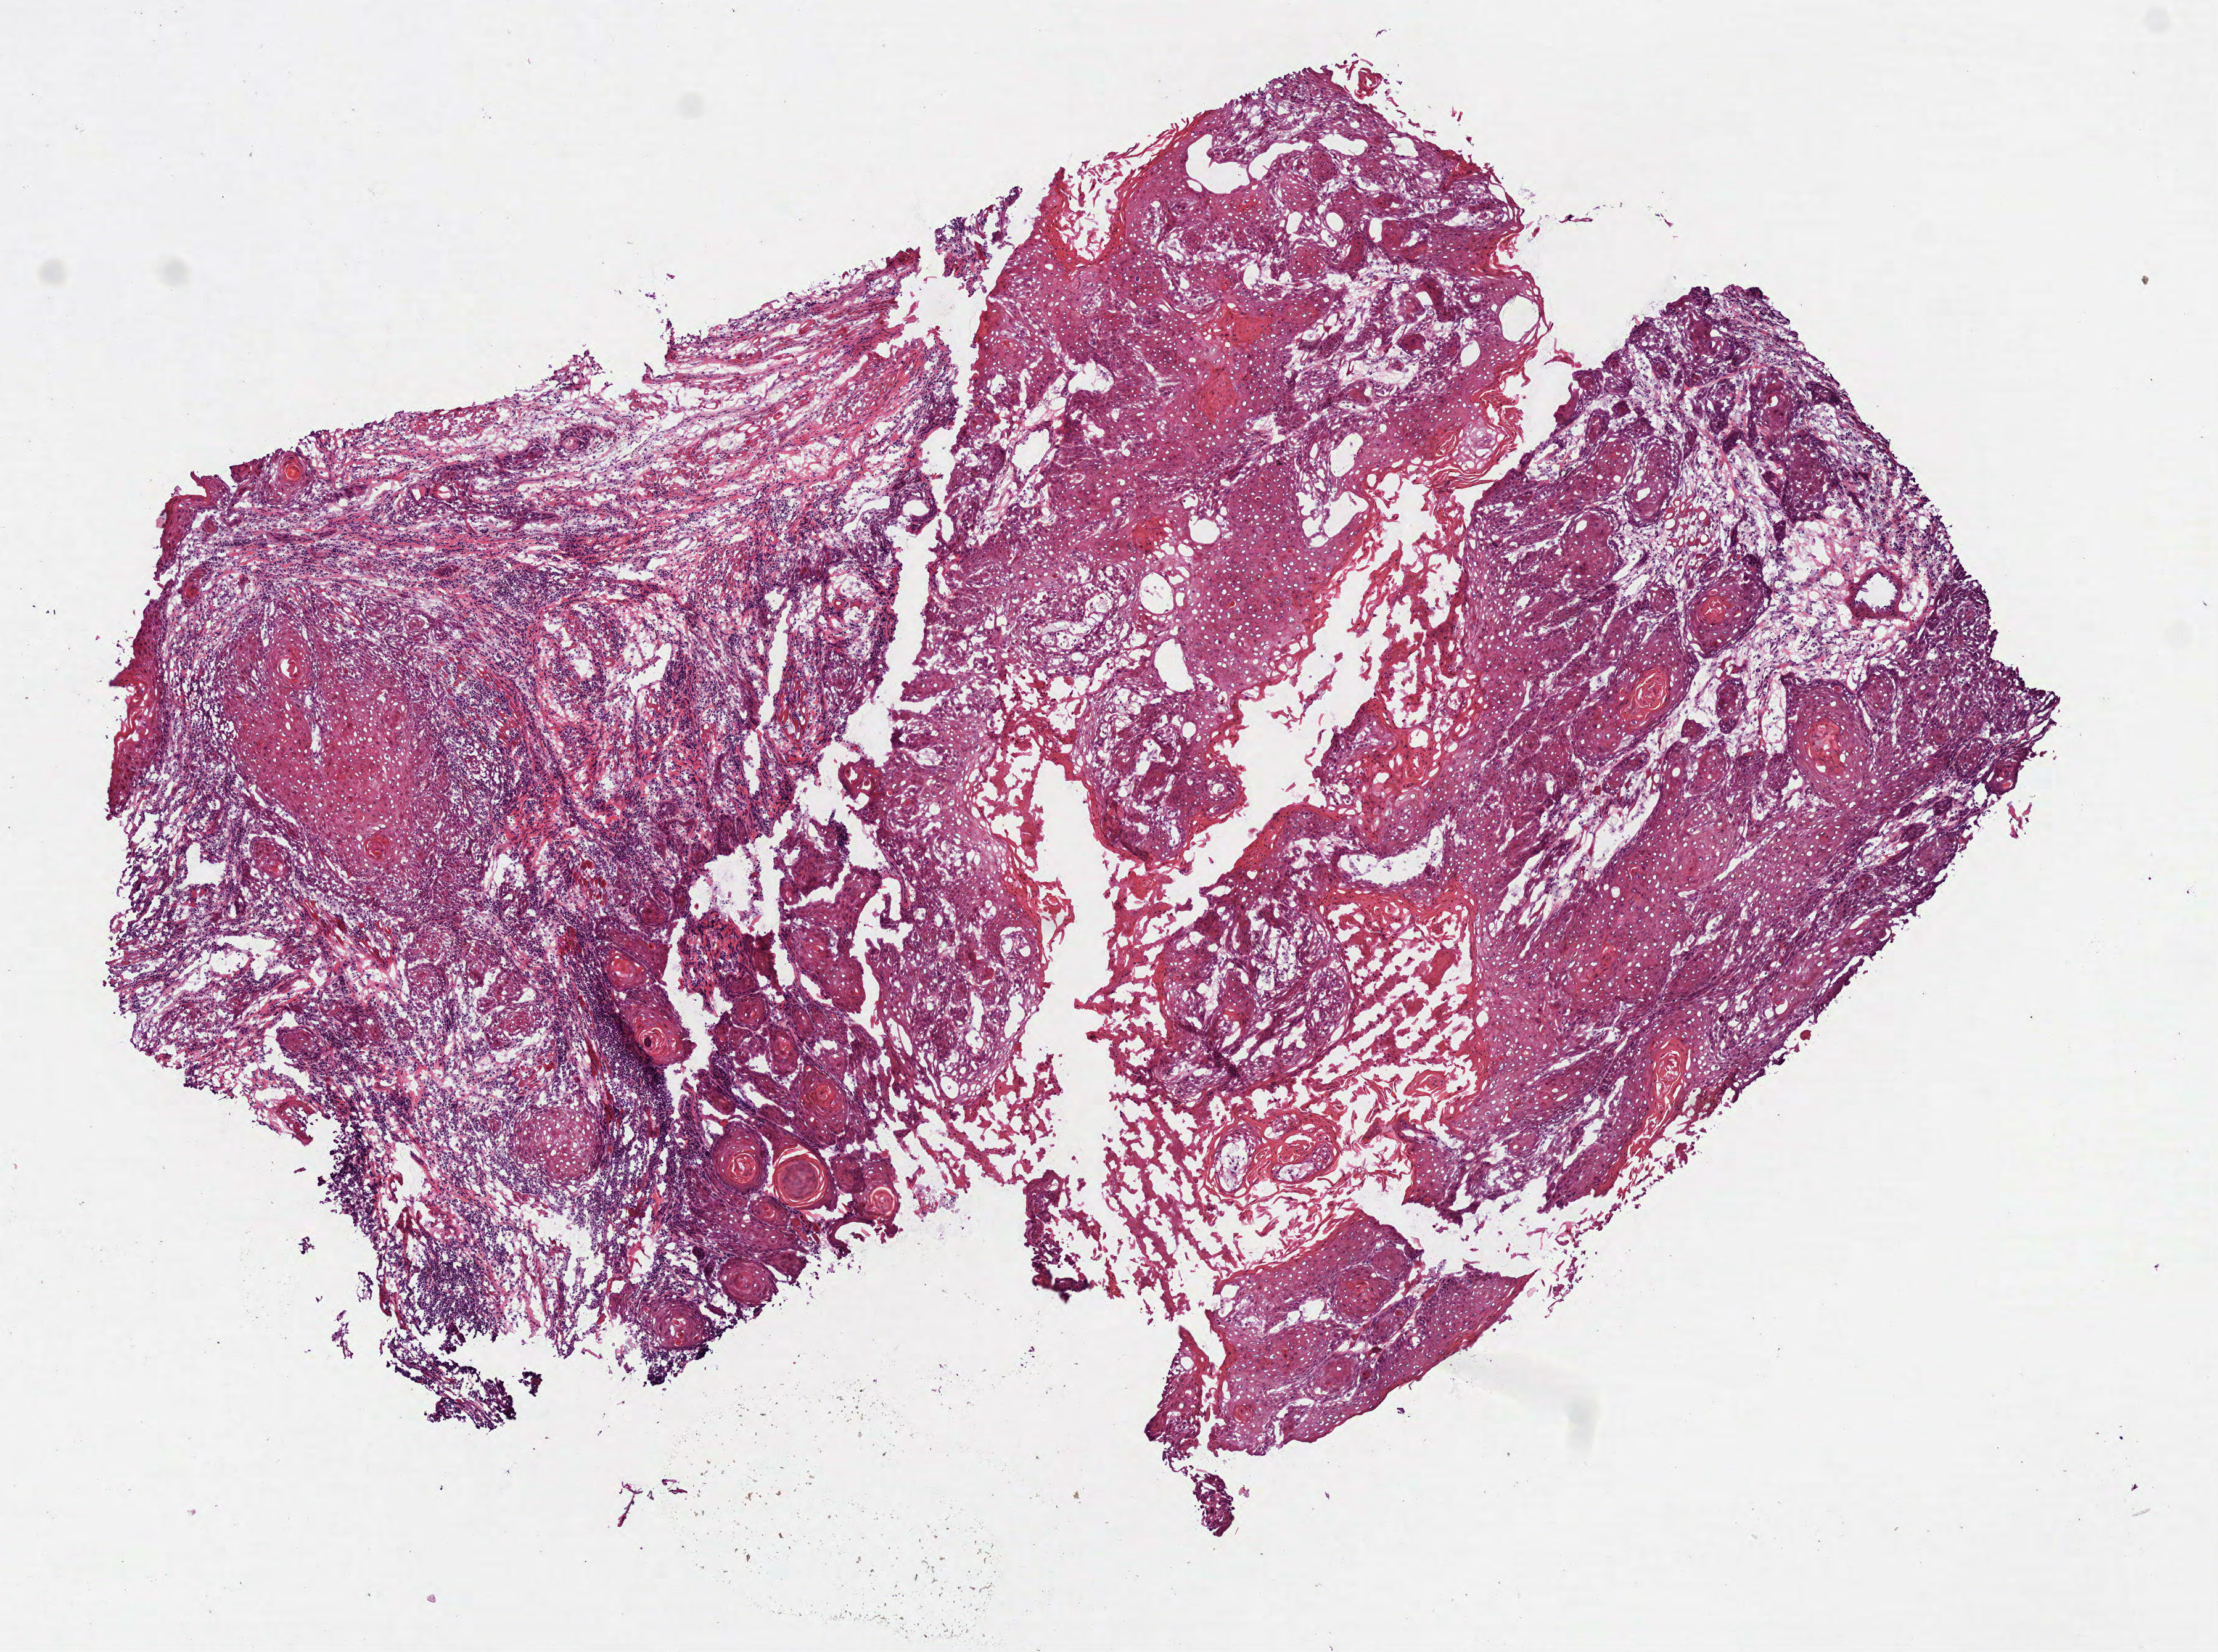
H&E-stained whole-slide image, a low-resolution overview of the entire scanned area, about 7.3 x 5.4 mm (slide scanned at 40x); frozen section; primary tumour sample from the head and neck. Female patient; age at initial diagnosis 65 years. Histologic grade: G1 (well differentiated). Pathologist review of this section (percent, as recorded): tumour cells 85%, tumour nuclei 60%, normal cells 0%, stromal cells 10%, necrosis 5%. Infiltration values recorded for this section: lymphocyte infiltration 30%, monocyte infiltration 0%, neutrophil infiltration 1%.
* histologic diagnosis: Squamous cell carcinoma, NOS
* AJCC pathologic stage: IVA (7th edition)